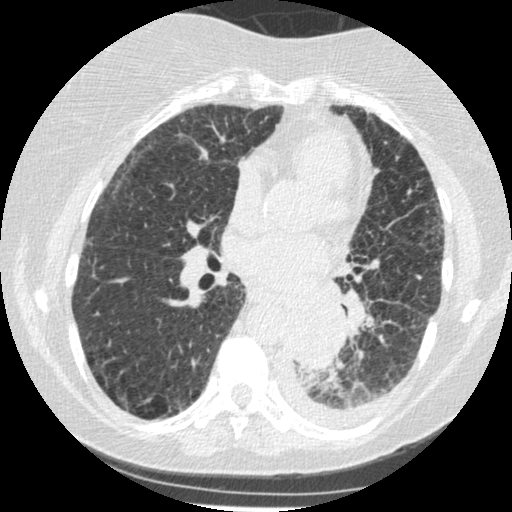
Low-dose screening chest CT, one axial slice. Position 117 of 341 along the scan axis. 120 kVp. Lung window (W 1500 / L -600 HU). 1.25 mm slice thickness. 512 × 512 image matrix.
Annotated regions visible in this slice (expert manual segmentation):
- lesion 1 (tumor, lower lobe of left lung): bounding box <284,301,344,368> (left, top, right, bottom; pixels)